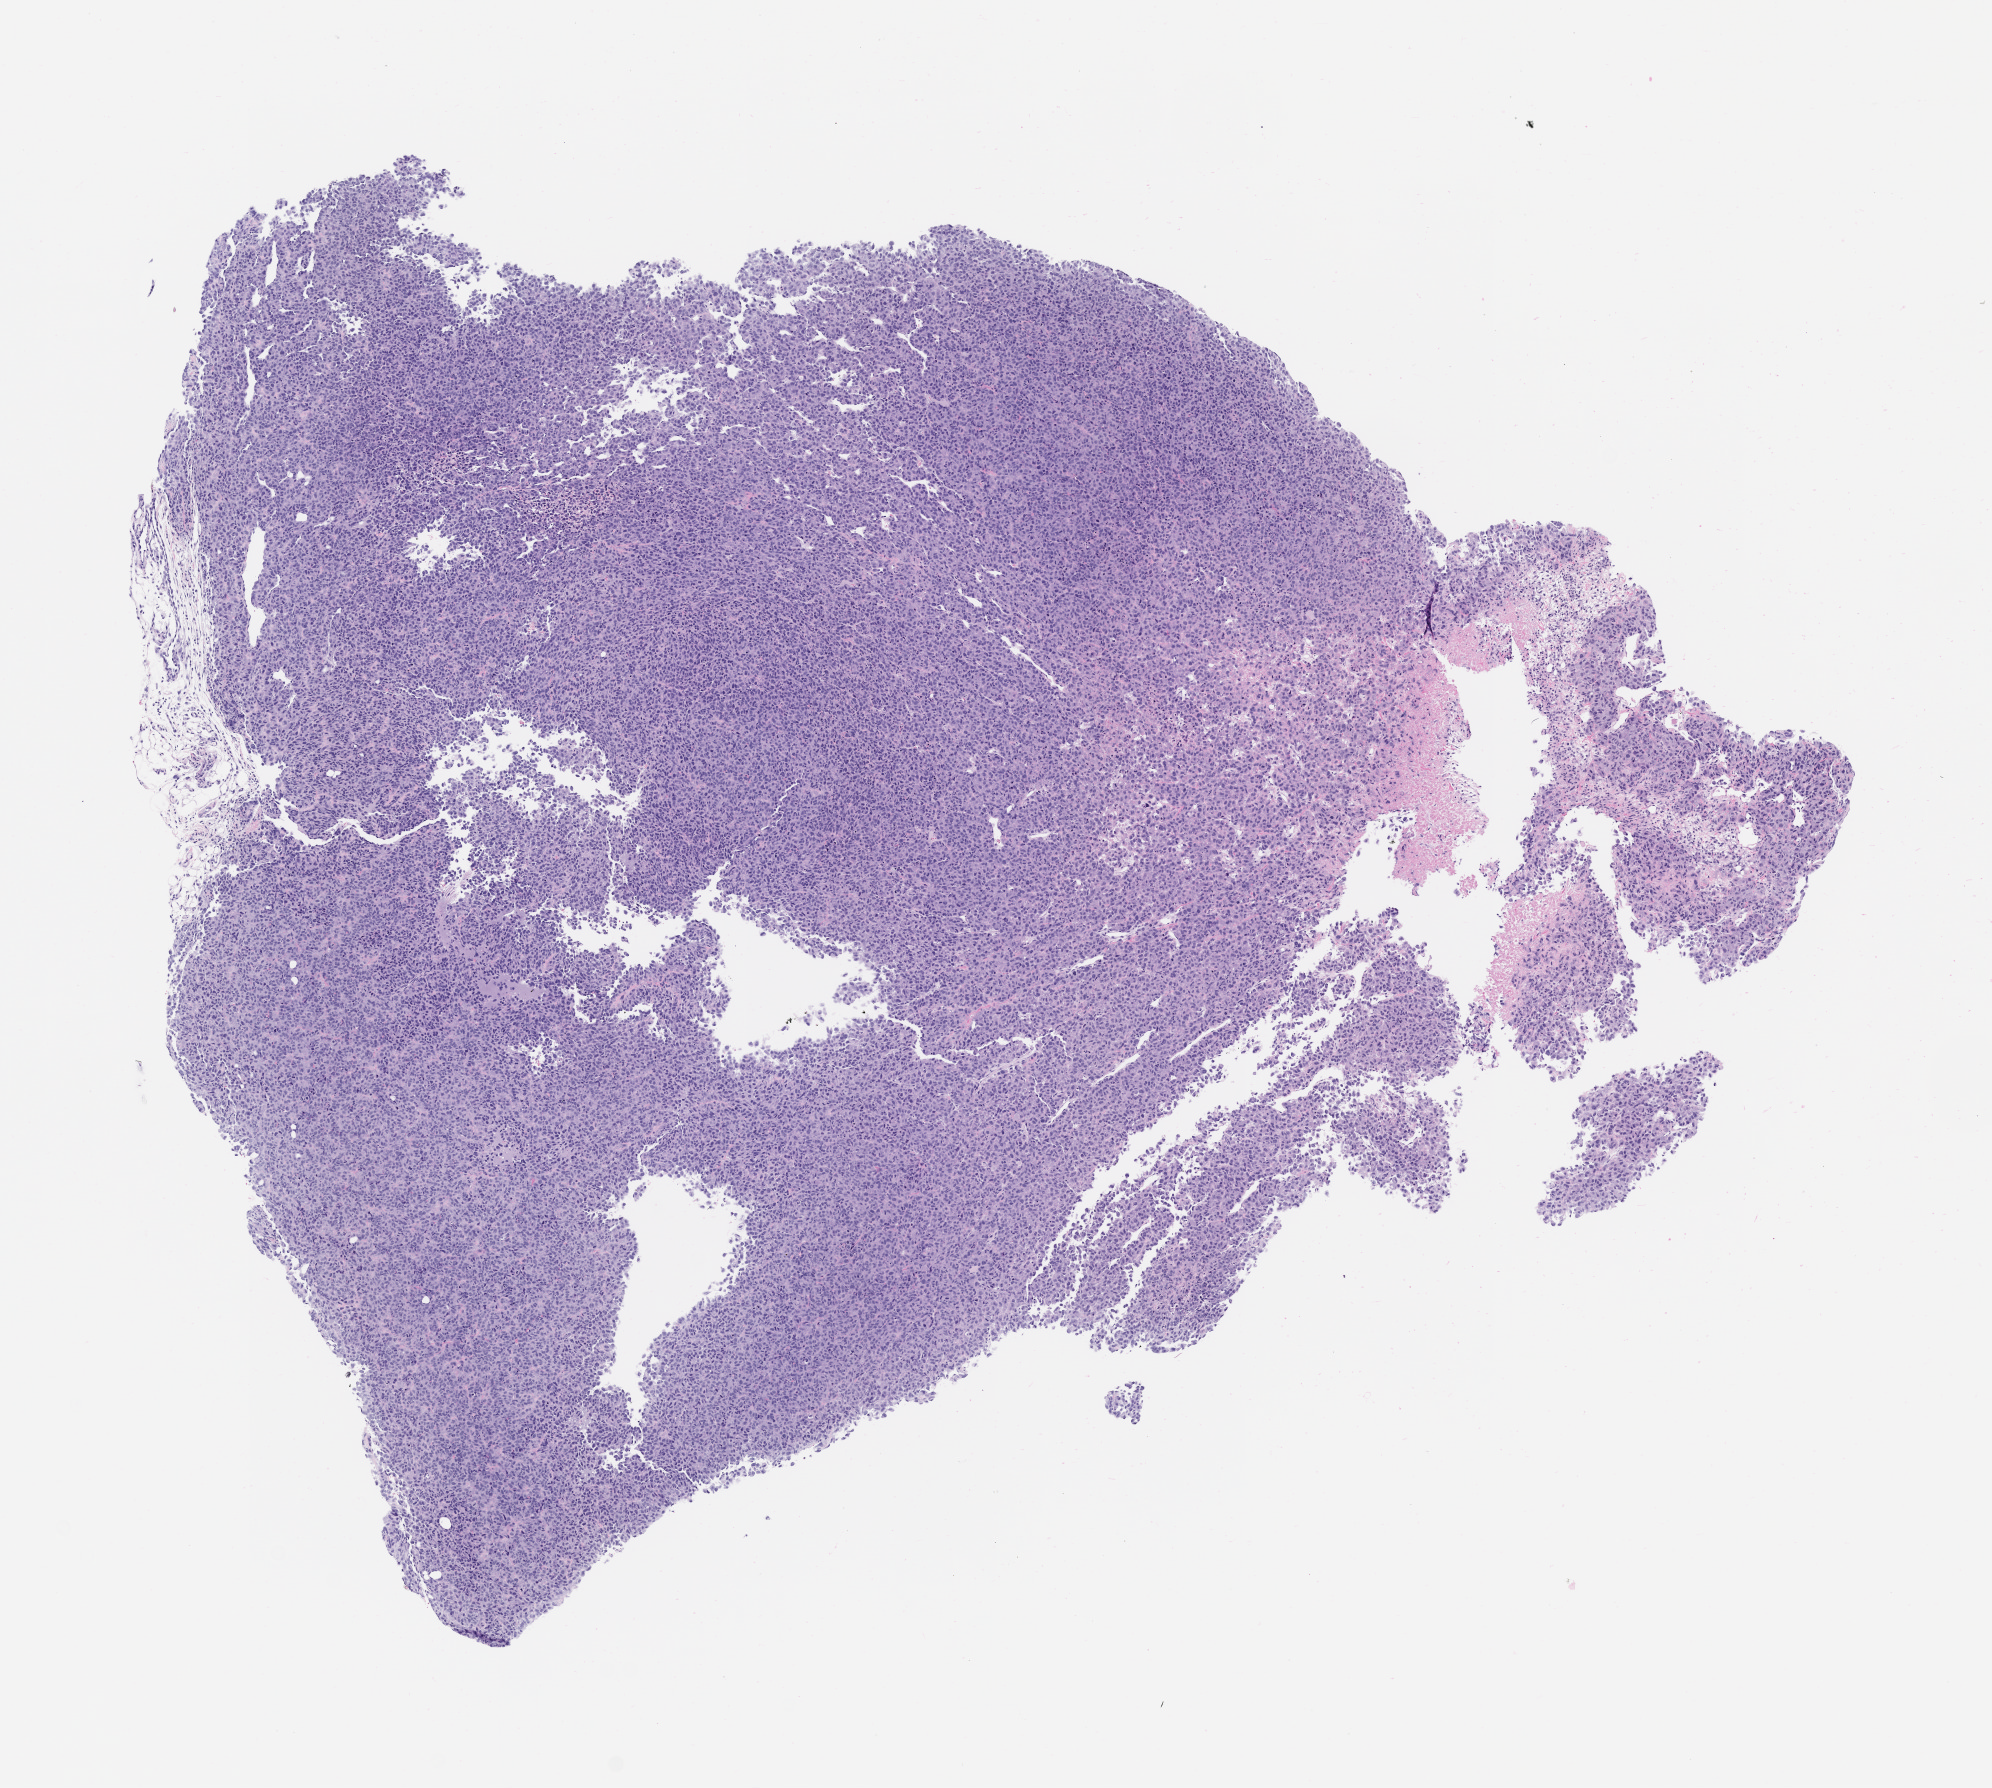
Hematoxylin and eosin (H&E) whole-slide image of a patient-derived xenograft (PDX) tumor grown in a mouse, passage 1 — low-resolution overview of the scanned area, about 8.0 x 7.2 mm. Formalin-fixed paraffin-embedded section. Originating tumor site category: bone.
Originating patient diagnosis: Osteosarcoma.